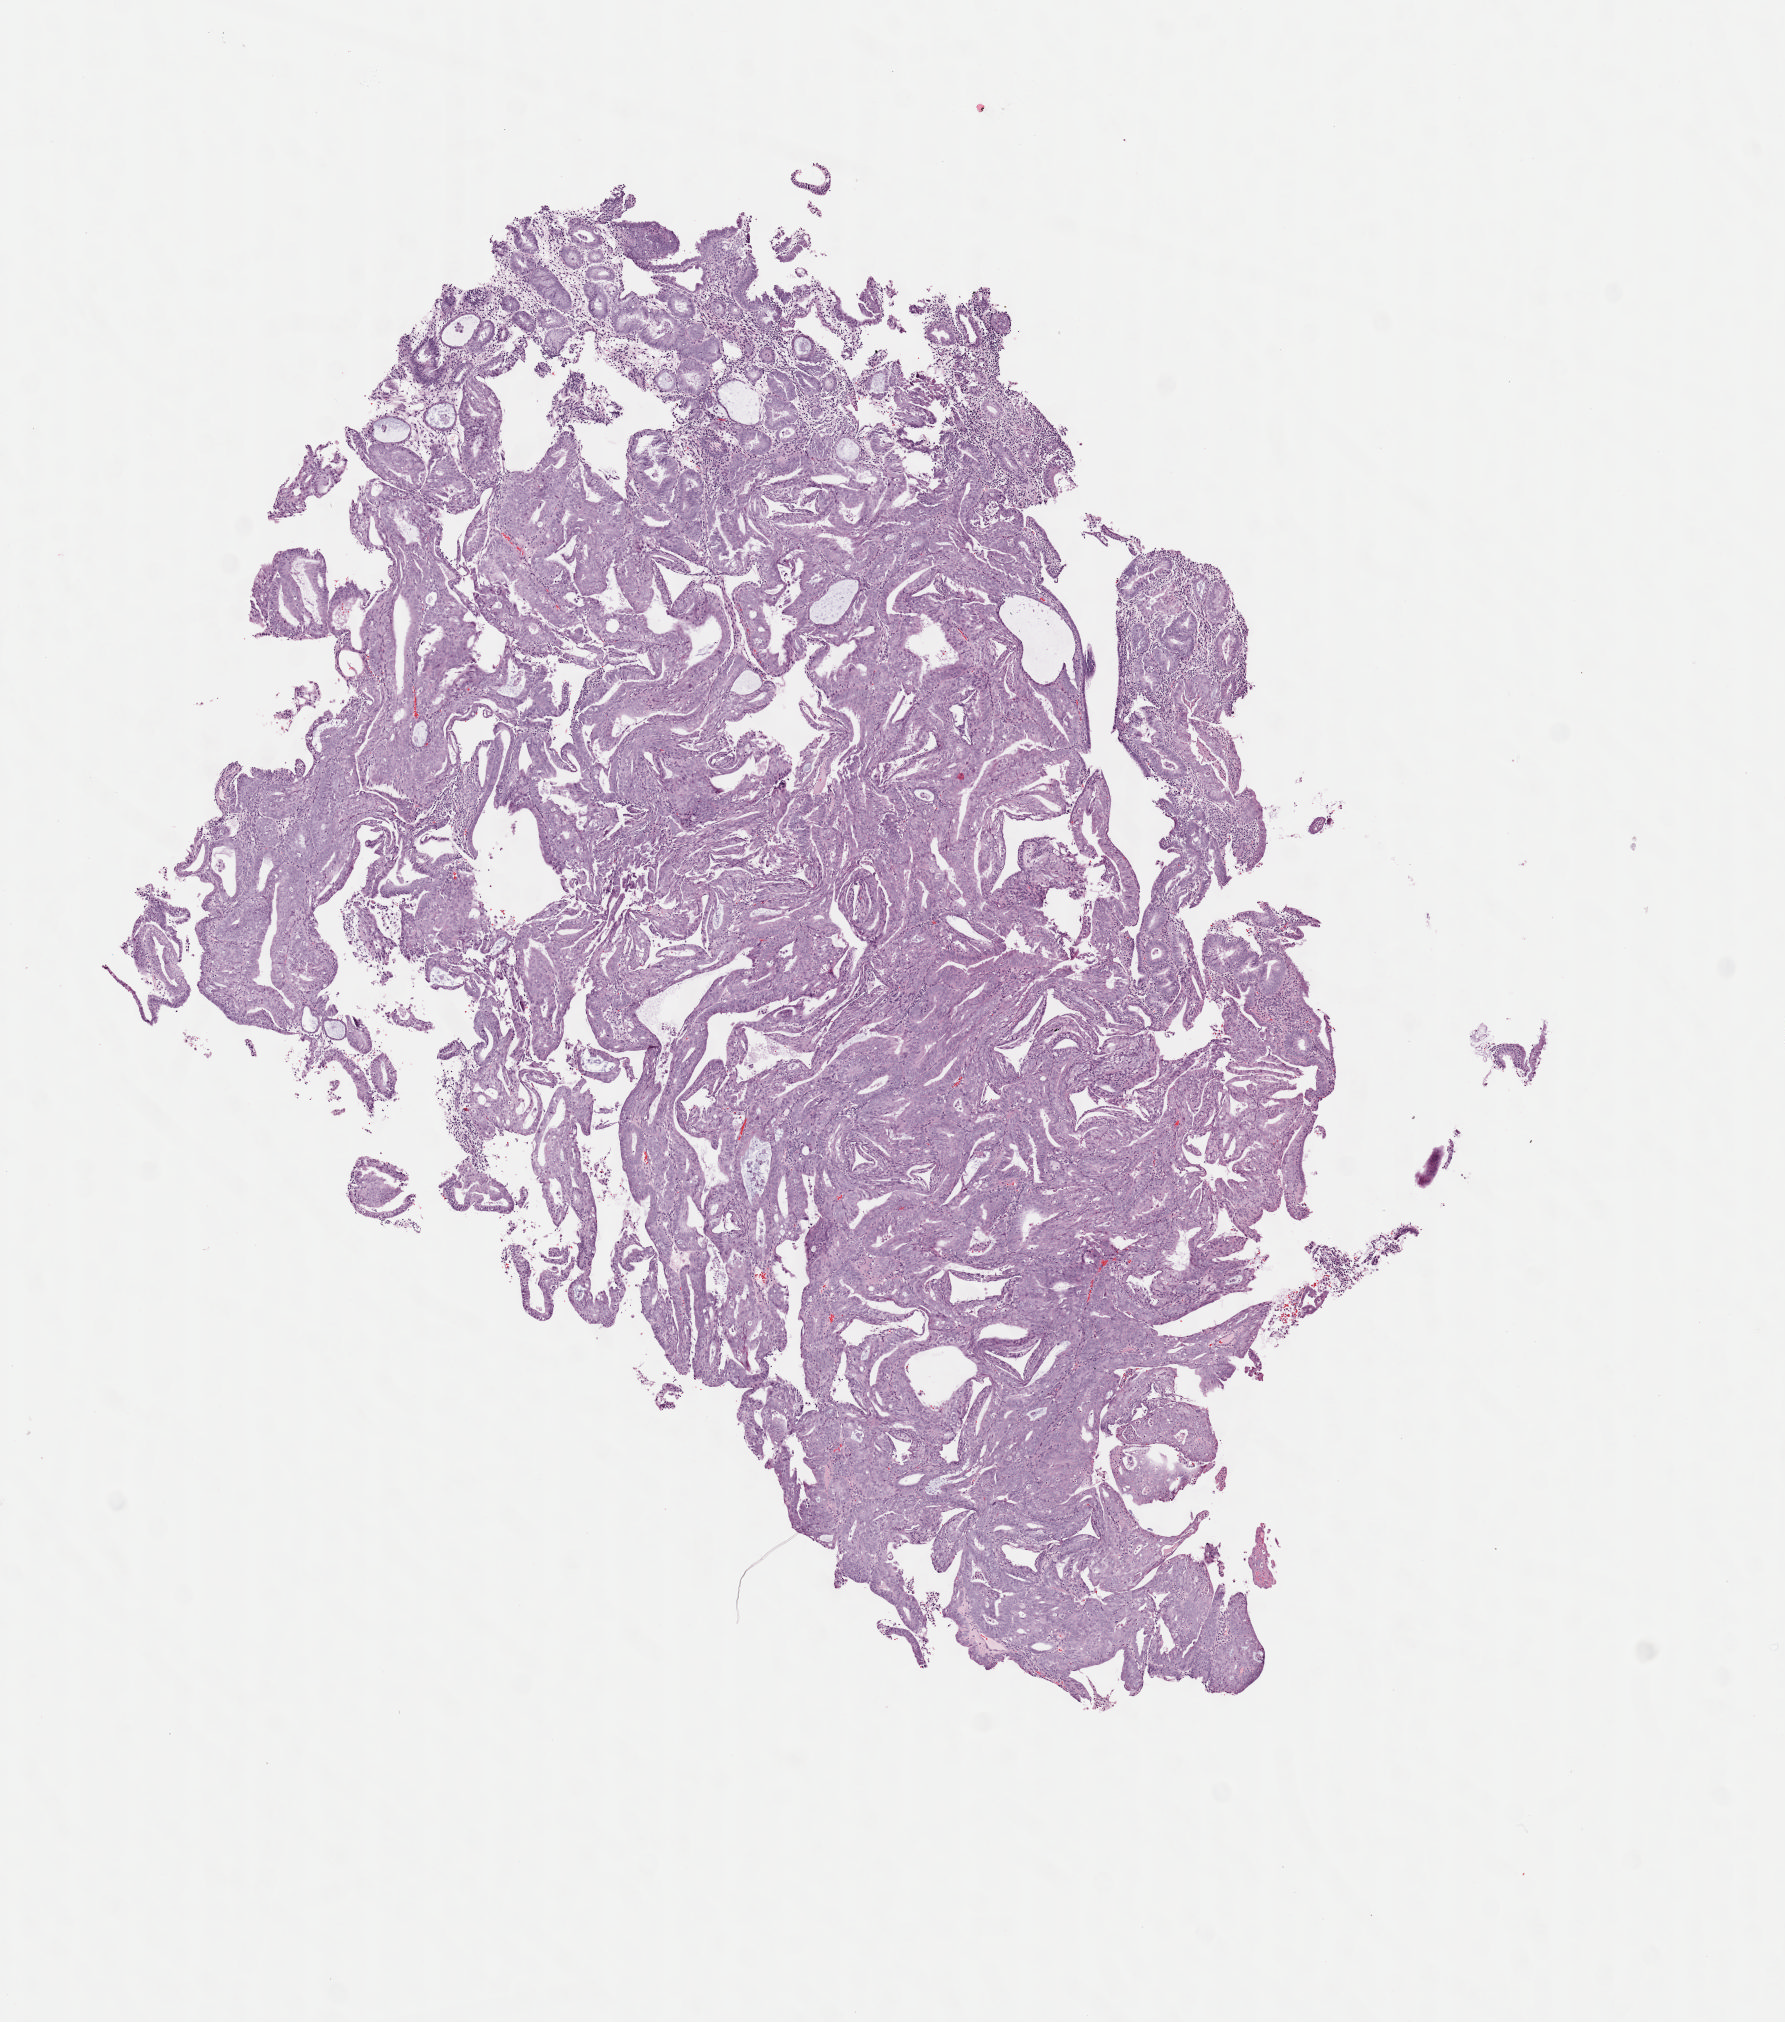
Digitized H&E-stained tissue section (whole slide), a low-resolution overview of the entire scanned area, about 7.0 x 8.0 mm (from a 40x scan). Frozen section. Uterus, primary tumour sample. Patient: female, age at initial diagnosis 61 years. Histologic grade: G3 (poorly differentiated). Slide review estimates, as recorded: tumour cells 99%, tumour nuclei 80%, normal cells 0%, stromal cells 0%, necrosis 1%. Infiltration values recorded for this section: lymphocyte infiltration 1%, monocyte infiltration 0%, neutrophil infiltration 0%.
* lymph nodes positive (case pathology): 9 of 14 examined
* diagnosis: Serous cystadenocarcinoma, NOS (endometrium)
* FIGO stage: IIIC